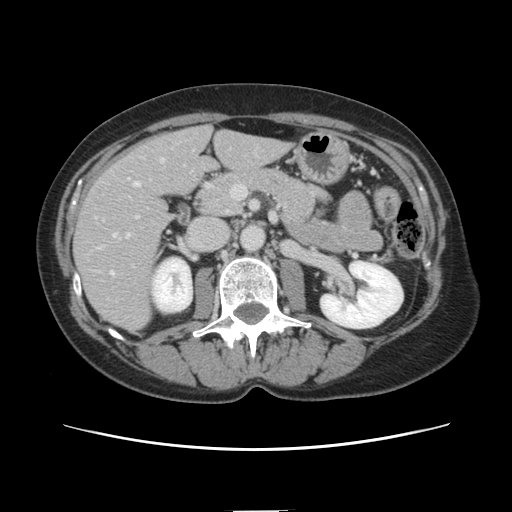
Contrast-enhanced abdominal CT, one axial slice. Slice 57 of 141 in the series (ordered by position). 120 kVp. Intravenous contrast given. Soft-tissue window (W 400 / L 40 HU). 2.5 mm slice thickness. 512 × 512 image matrix, field of view 350 × 350 mm. Female patient, age 63 years. From the clinical record (not read from this slice): diagnosis: colorectal cancer liver metastases, imaged before liver resection; multiple liver metastases: yes; largest metastasis: 3.2 cm; disease in both lobes: yes.
Structures marked on this image (expert manual segmentation):
- hepatic veins: bounding box (x1, y1, x2, y2) in pixels: (110, 159, 163, 276)
- liver: (75, 126, 288, 331)
- planned liver remnant (the part of the liver to remain after resection): (177, 127, 288, 185)
- portal vein (with intrahepatic branches): (127, 178, 130, 236)